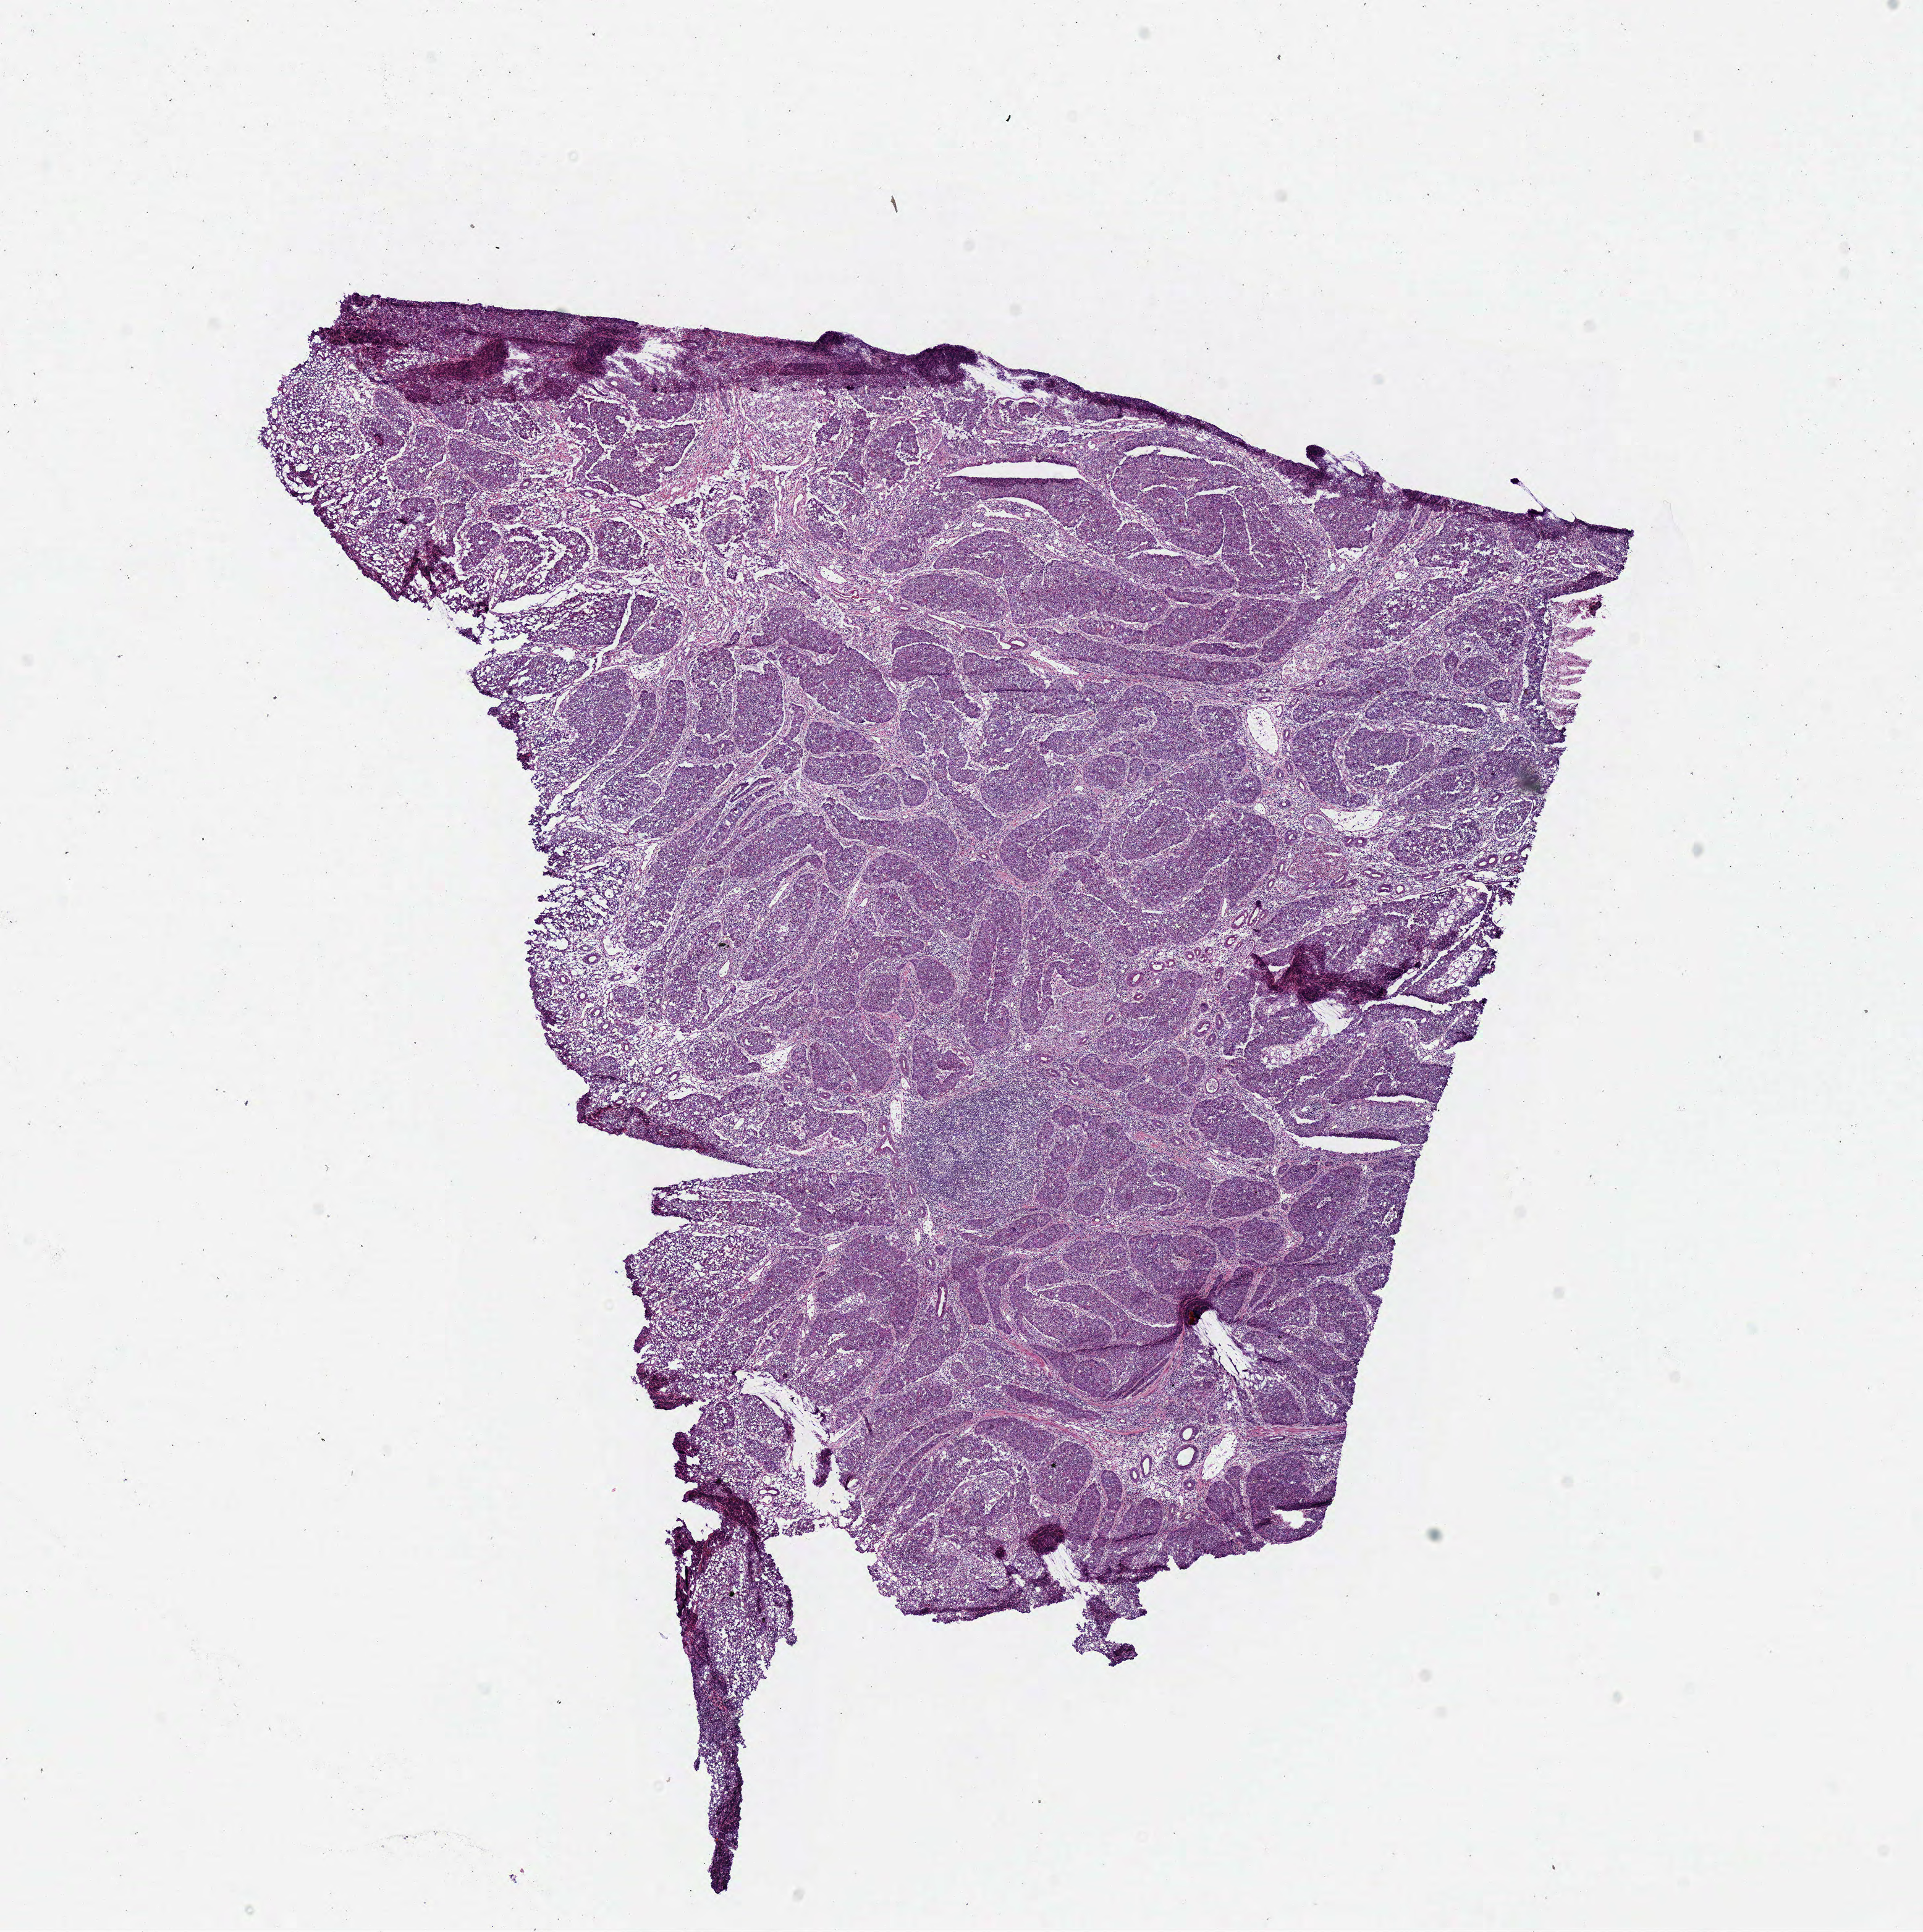
H&E-stained whole-slide image — shown as a low-resolution overview of the whole scanned area (about 12.2 x 12.3 mm, slide scanned at 40x), frozen section from the bottom of the tissue portion, colon, primary tumour sample. Patient: female, age at initial diagnosis 70 years. Composition of this section per pathologist review: tumour cells 77%, tumour nuclei 75%, normal cells 3%, stromal cells 15%, necrosis 5%.
• TNM: T3 N0 M0
• lymph nodes positive (case pathology): 0 of 23 examined
• histologic diagnosis: Adenocarcinoma, NOS (cecum)
• AJCC pathologic stage: II (6th edition)